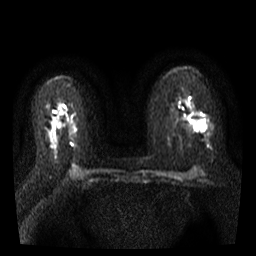
Breast MRI, one axial slice; slice 16 of 35 in the series (ordered by position); diffusion-weighted series; image 2 of 4 stored at this slice position (different b-values; order by instance number); 3 T; 256 × 256 image matrix. Female patient.
Annotated regions visible in this slice (outlined manually by an expert reader):
- tumour on diffusion-weighted imaging: box from (x=193, y=118) to (x=207, y=132) px